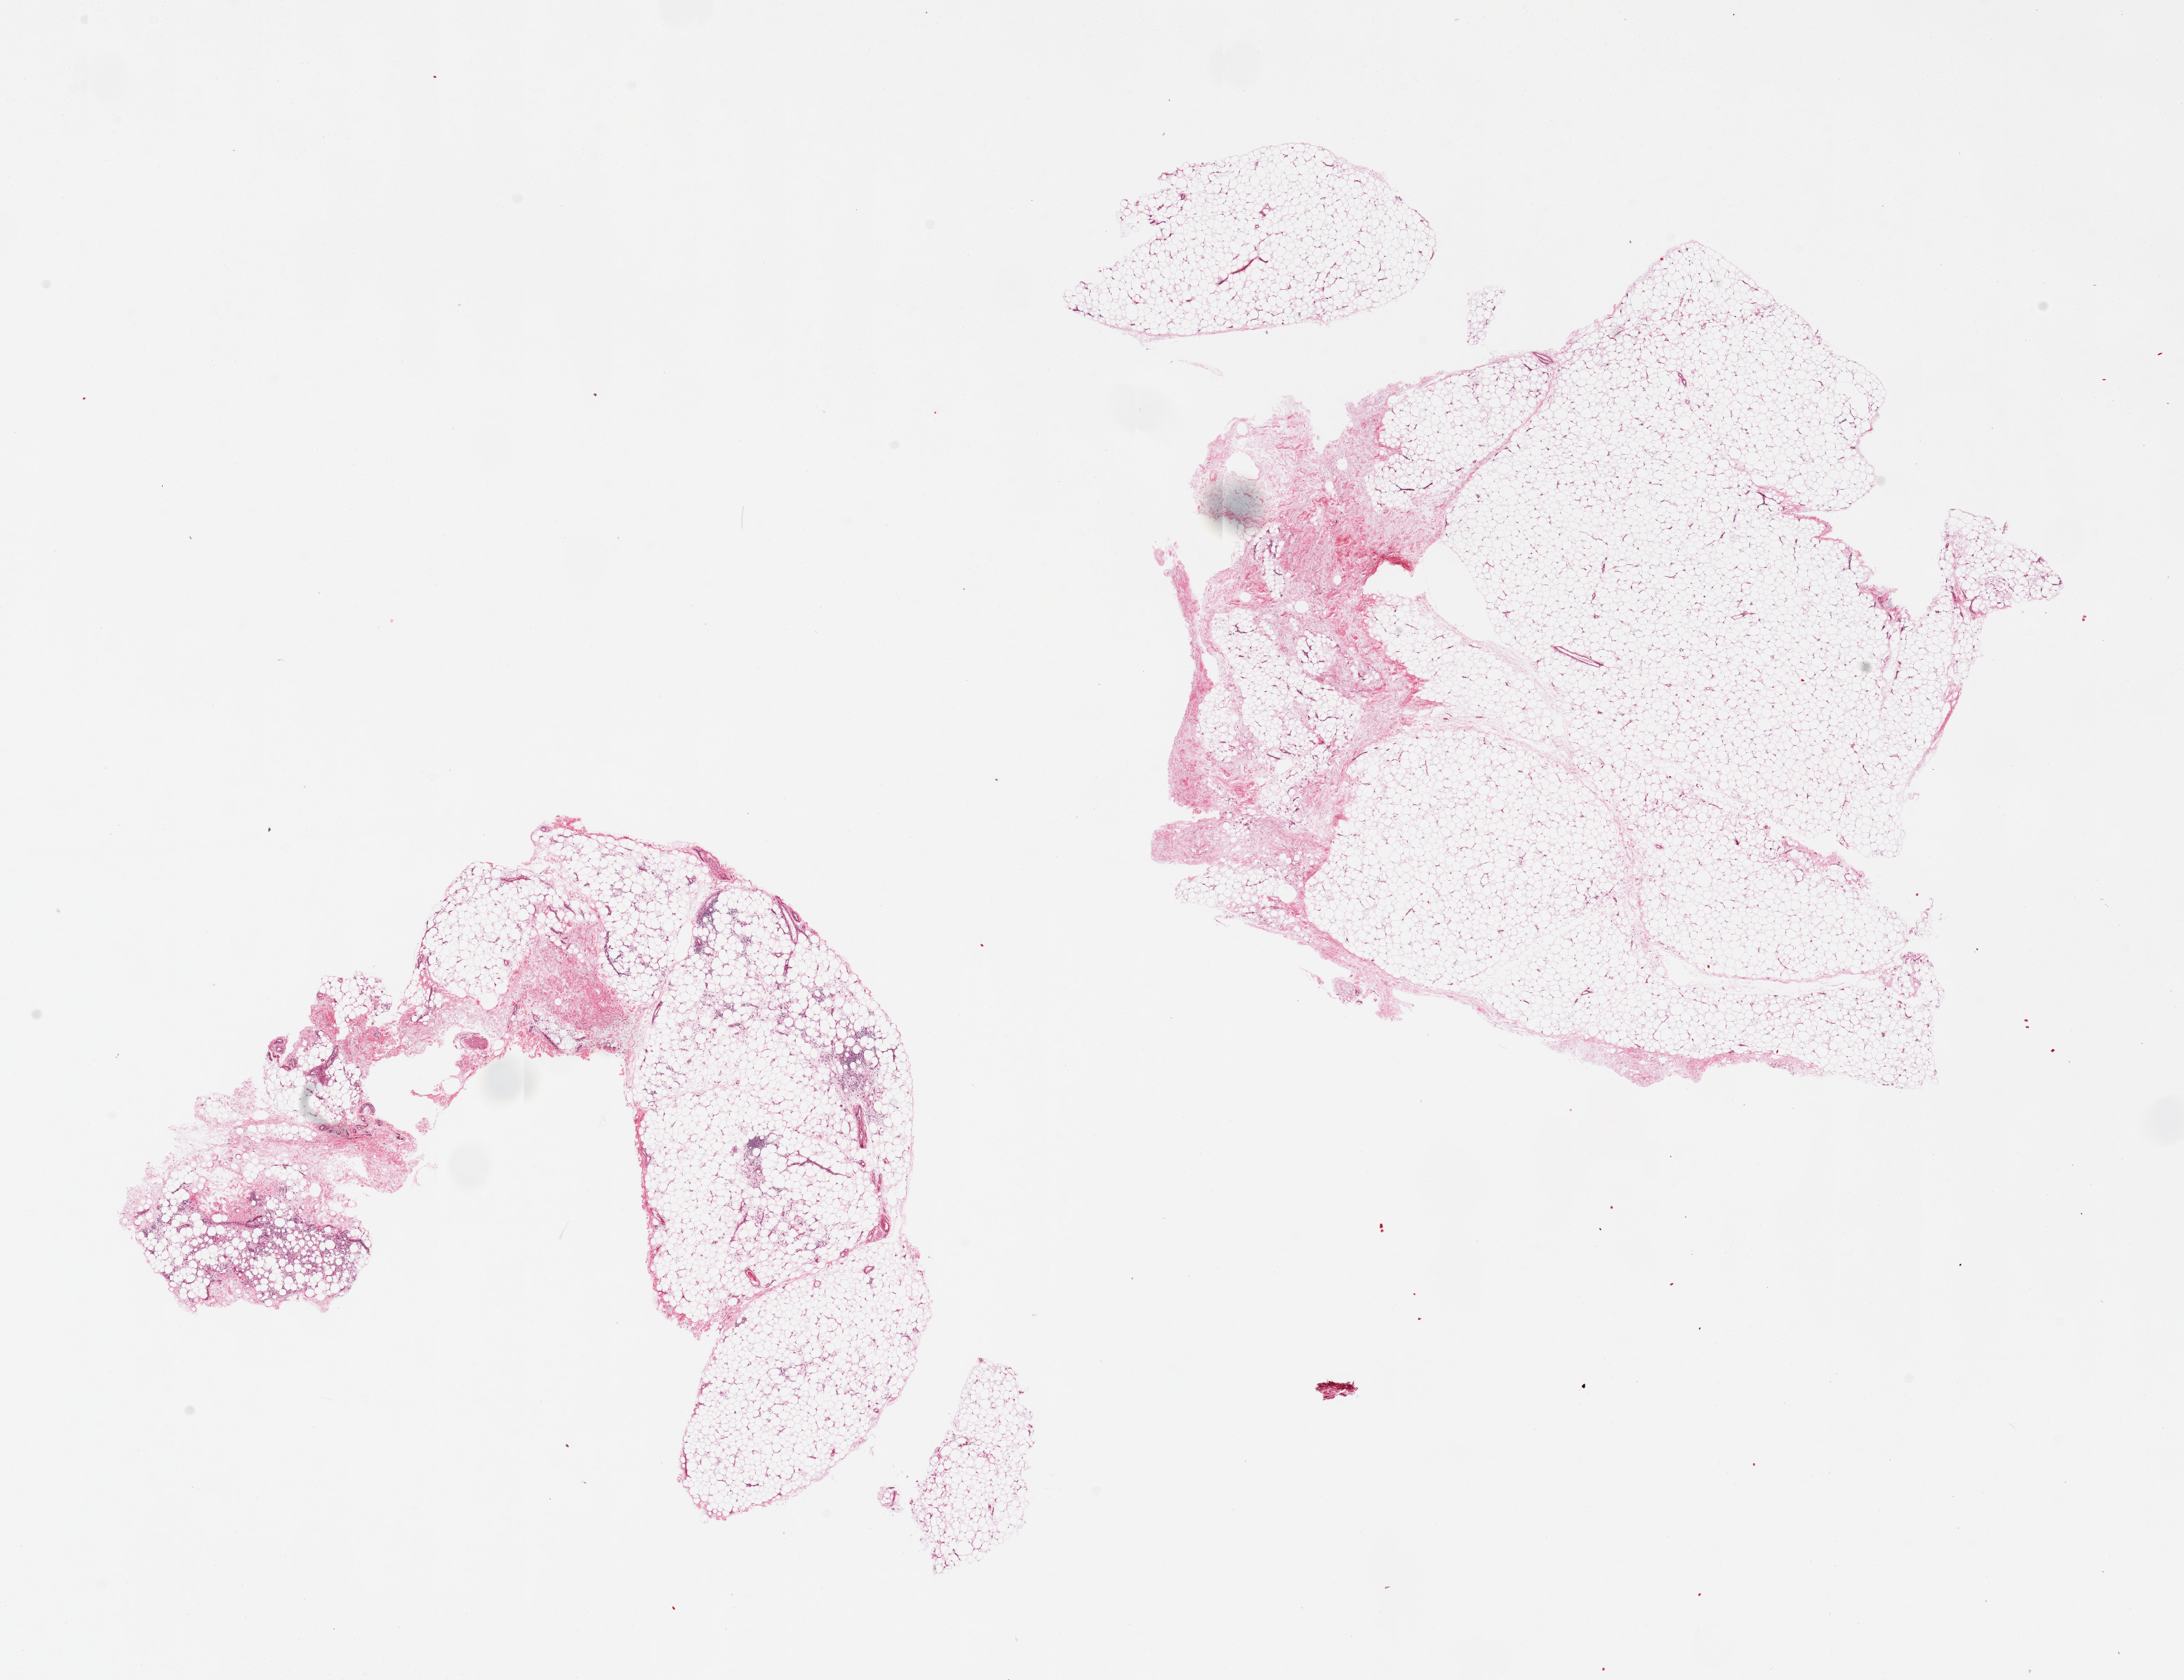
Hematoxylin and eosin (H&E) whole-slide image — shown as a low-resolution overview of the whole scanned area (about 24.6 x 18.9 mm, slide scanned at 20x); PAXgene-fixed paraffin-embedded (PFPE) section; sampled site (target tissue): adipose tissue; tissue donor sample.
Review note (as recorded): 2 pieces.